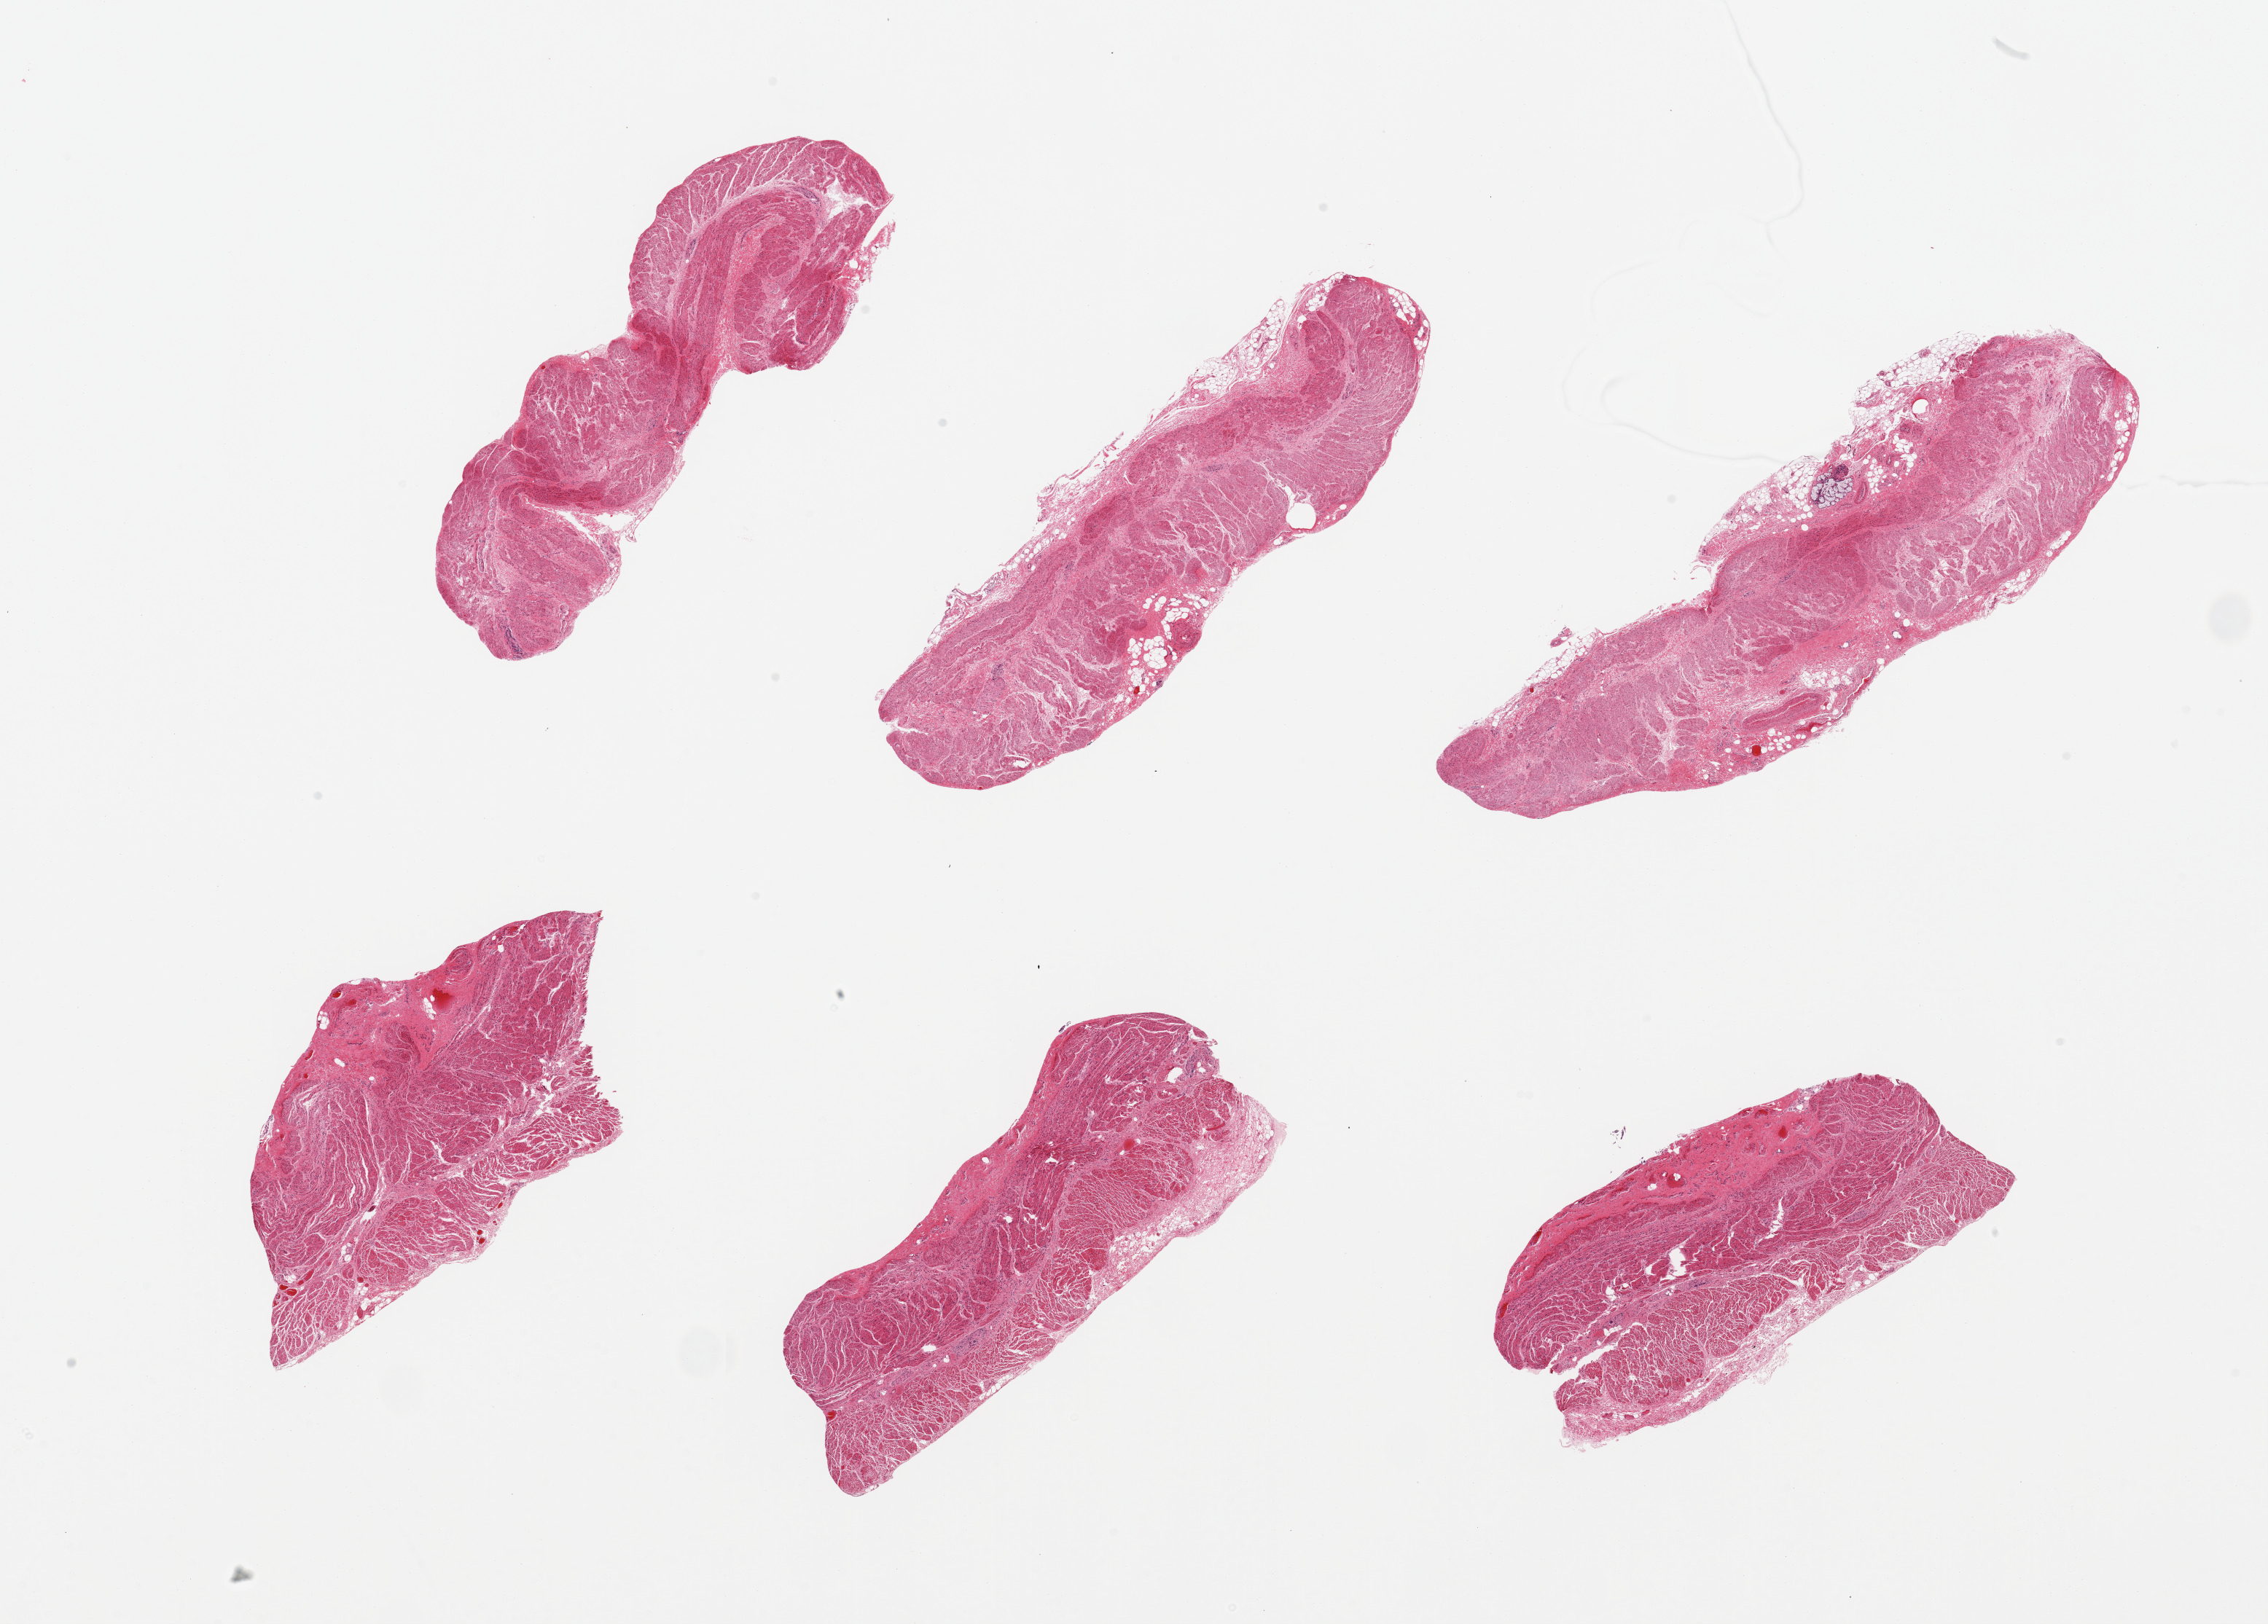
Whole-slide image, haematoxylin and eosin stain — whole scanned area (about 24.6 x 17.6 mm) shown as a low-resolution overview; PAXgene-fixed, paraffin-embedded tissue; section of gastroesophageal junction (target tissue); tissue donor sample. Male donor.
Review note (as recorded): 6 pieces; 0.5 mm submucosal gland in 1.